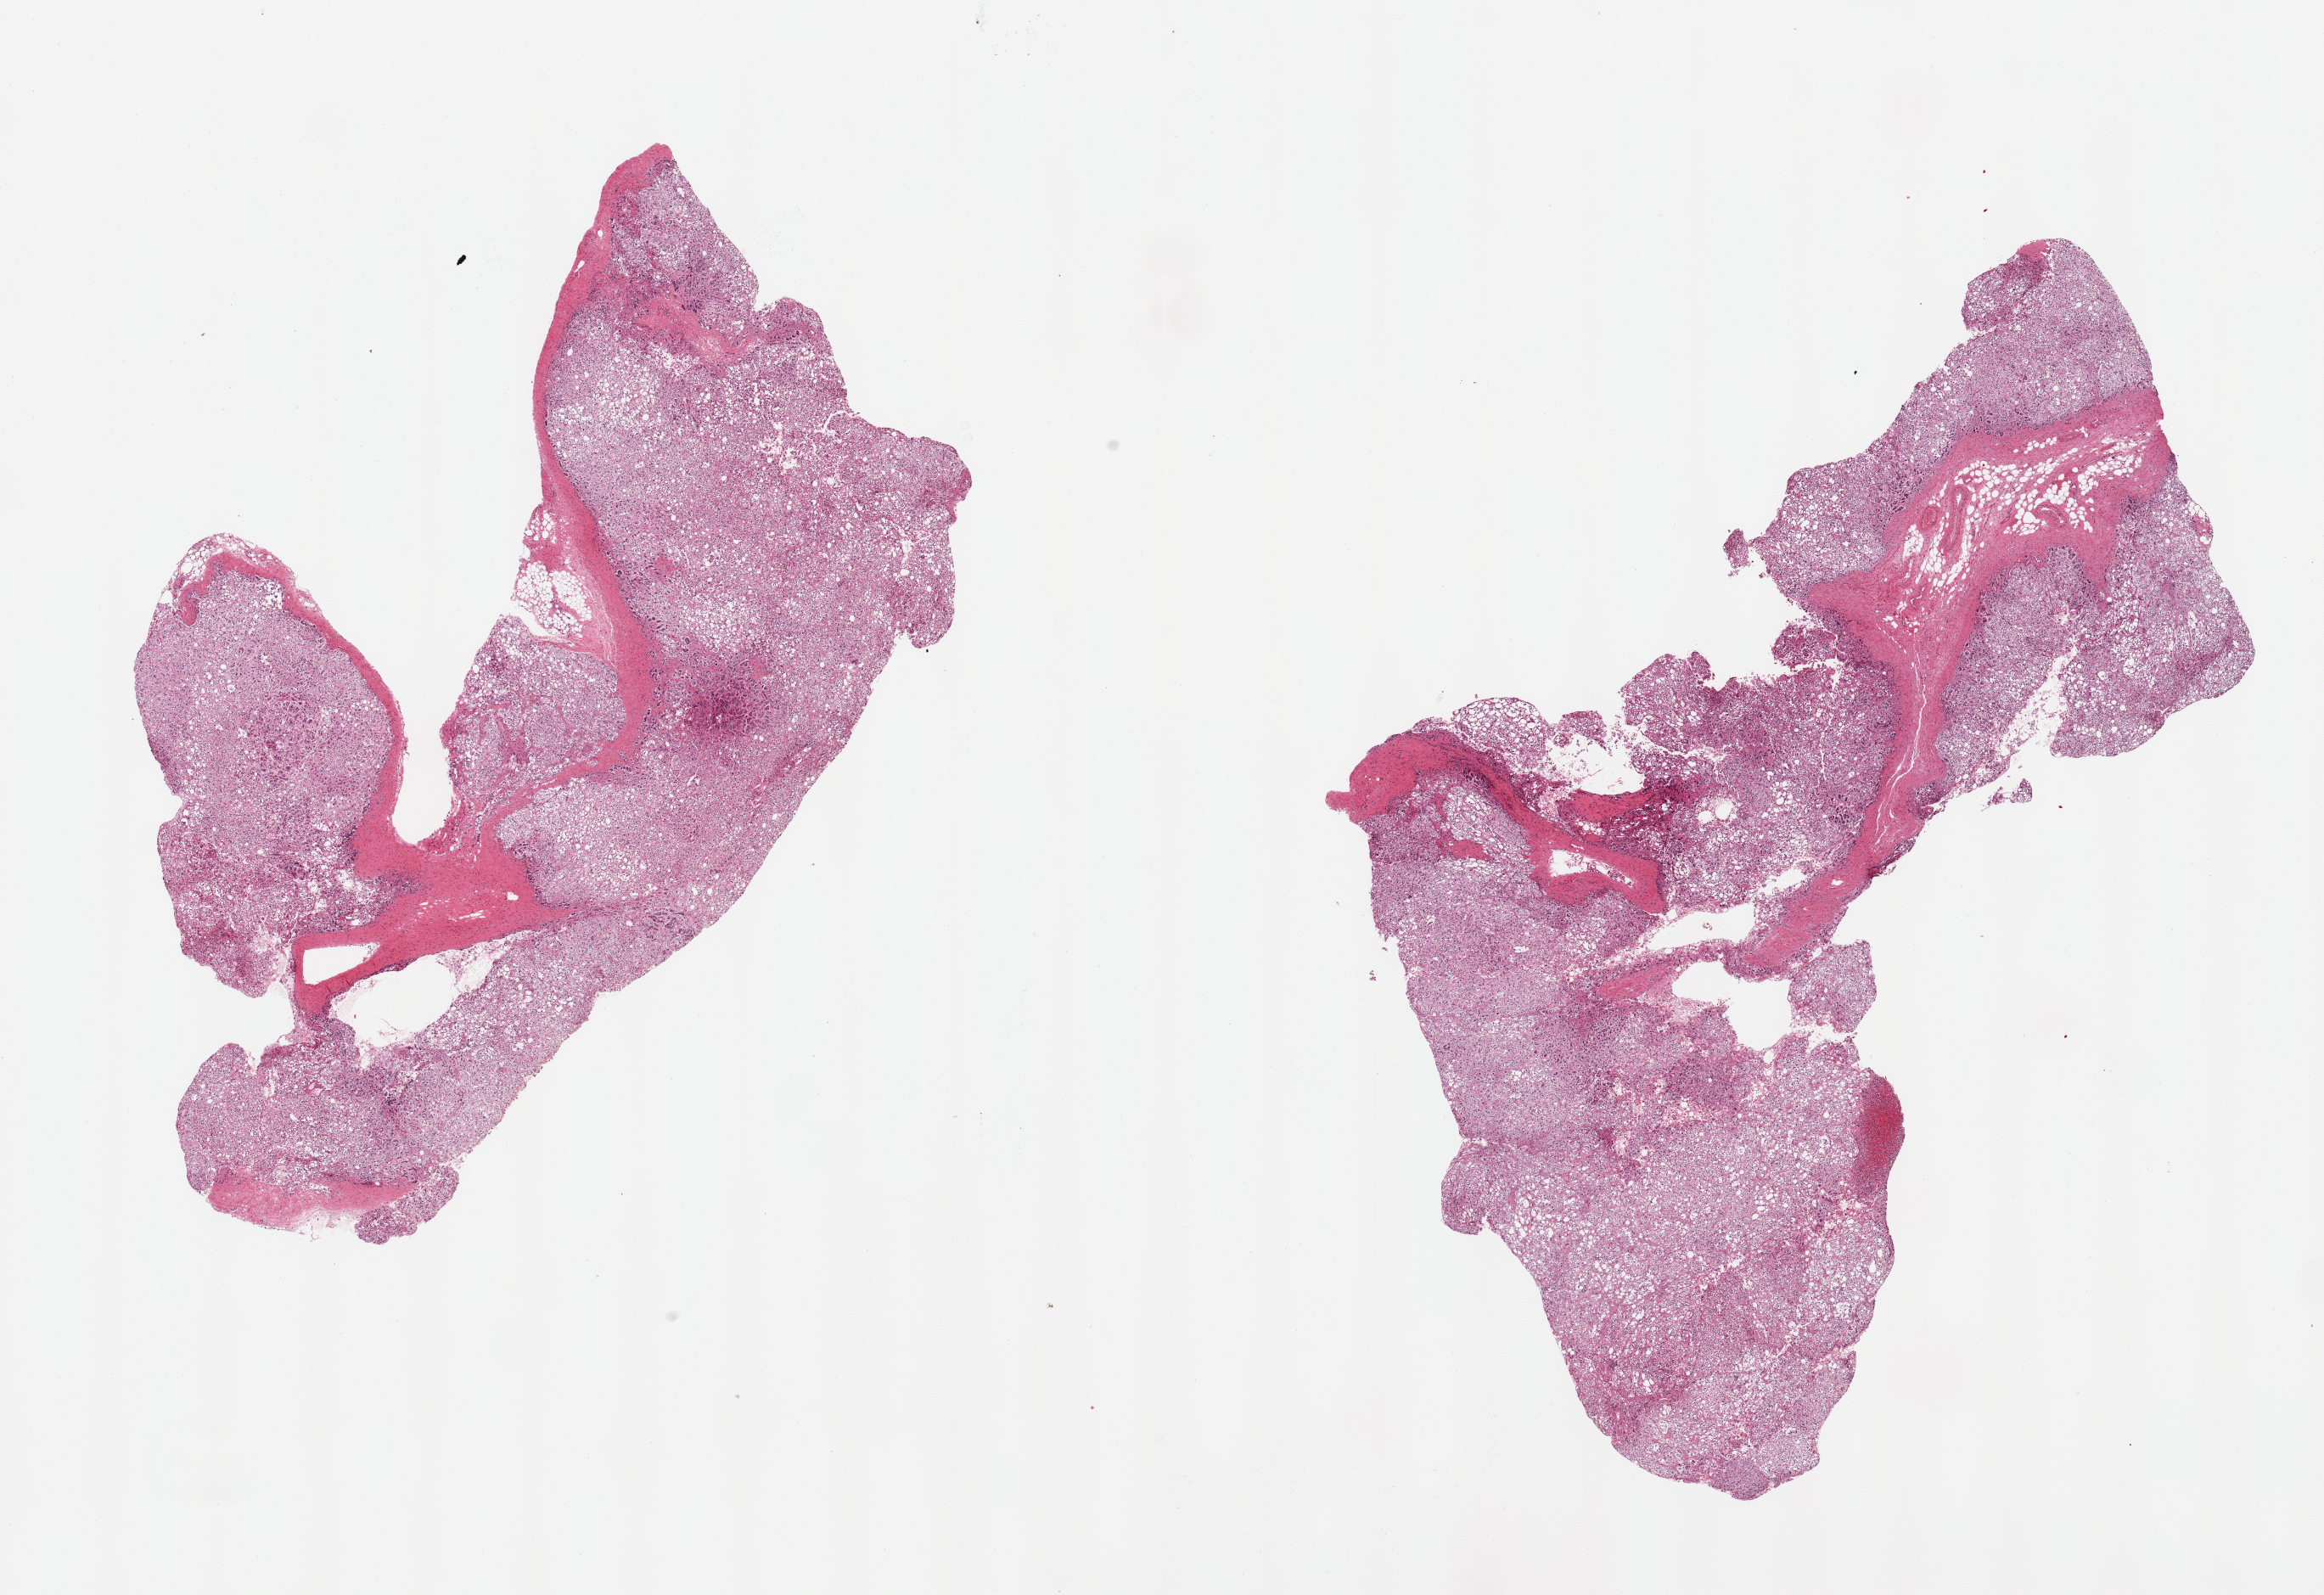
Haematoxylin and eosin whole-slide image — whole scanned area (about 21.7 x 14.9 mm, acquisition: 20x scan) shown as a low-resolution overview; PAXgene-fixed, paraffin-embedded tissue; target tissue: adrenal gland; tissue donor sample. Donor: female.
Reviewer comment on this tissue sample: 2 pieces.